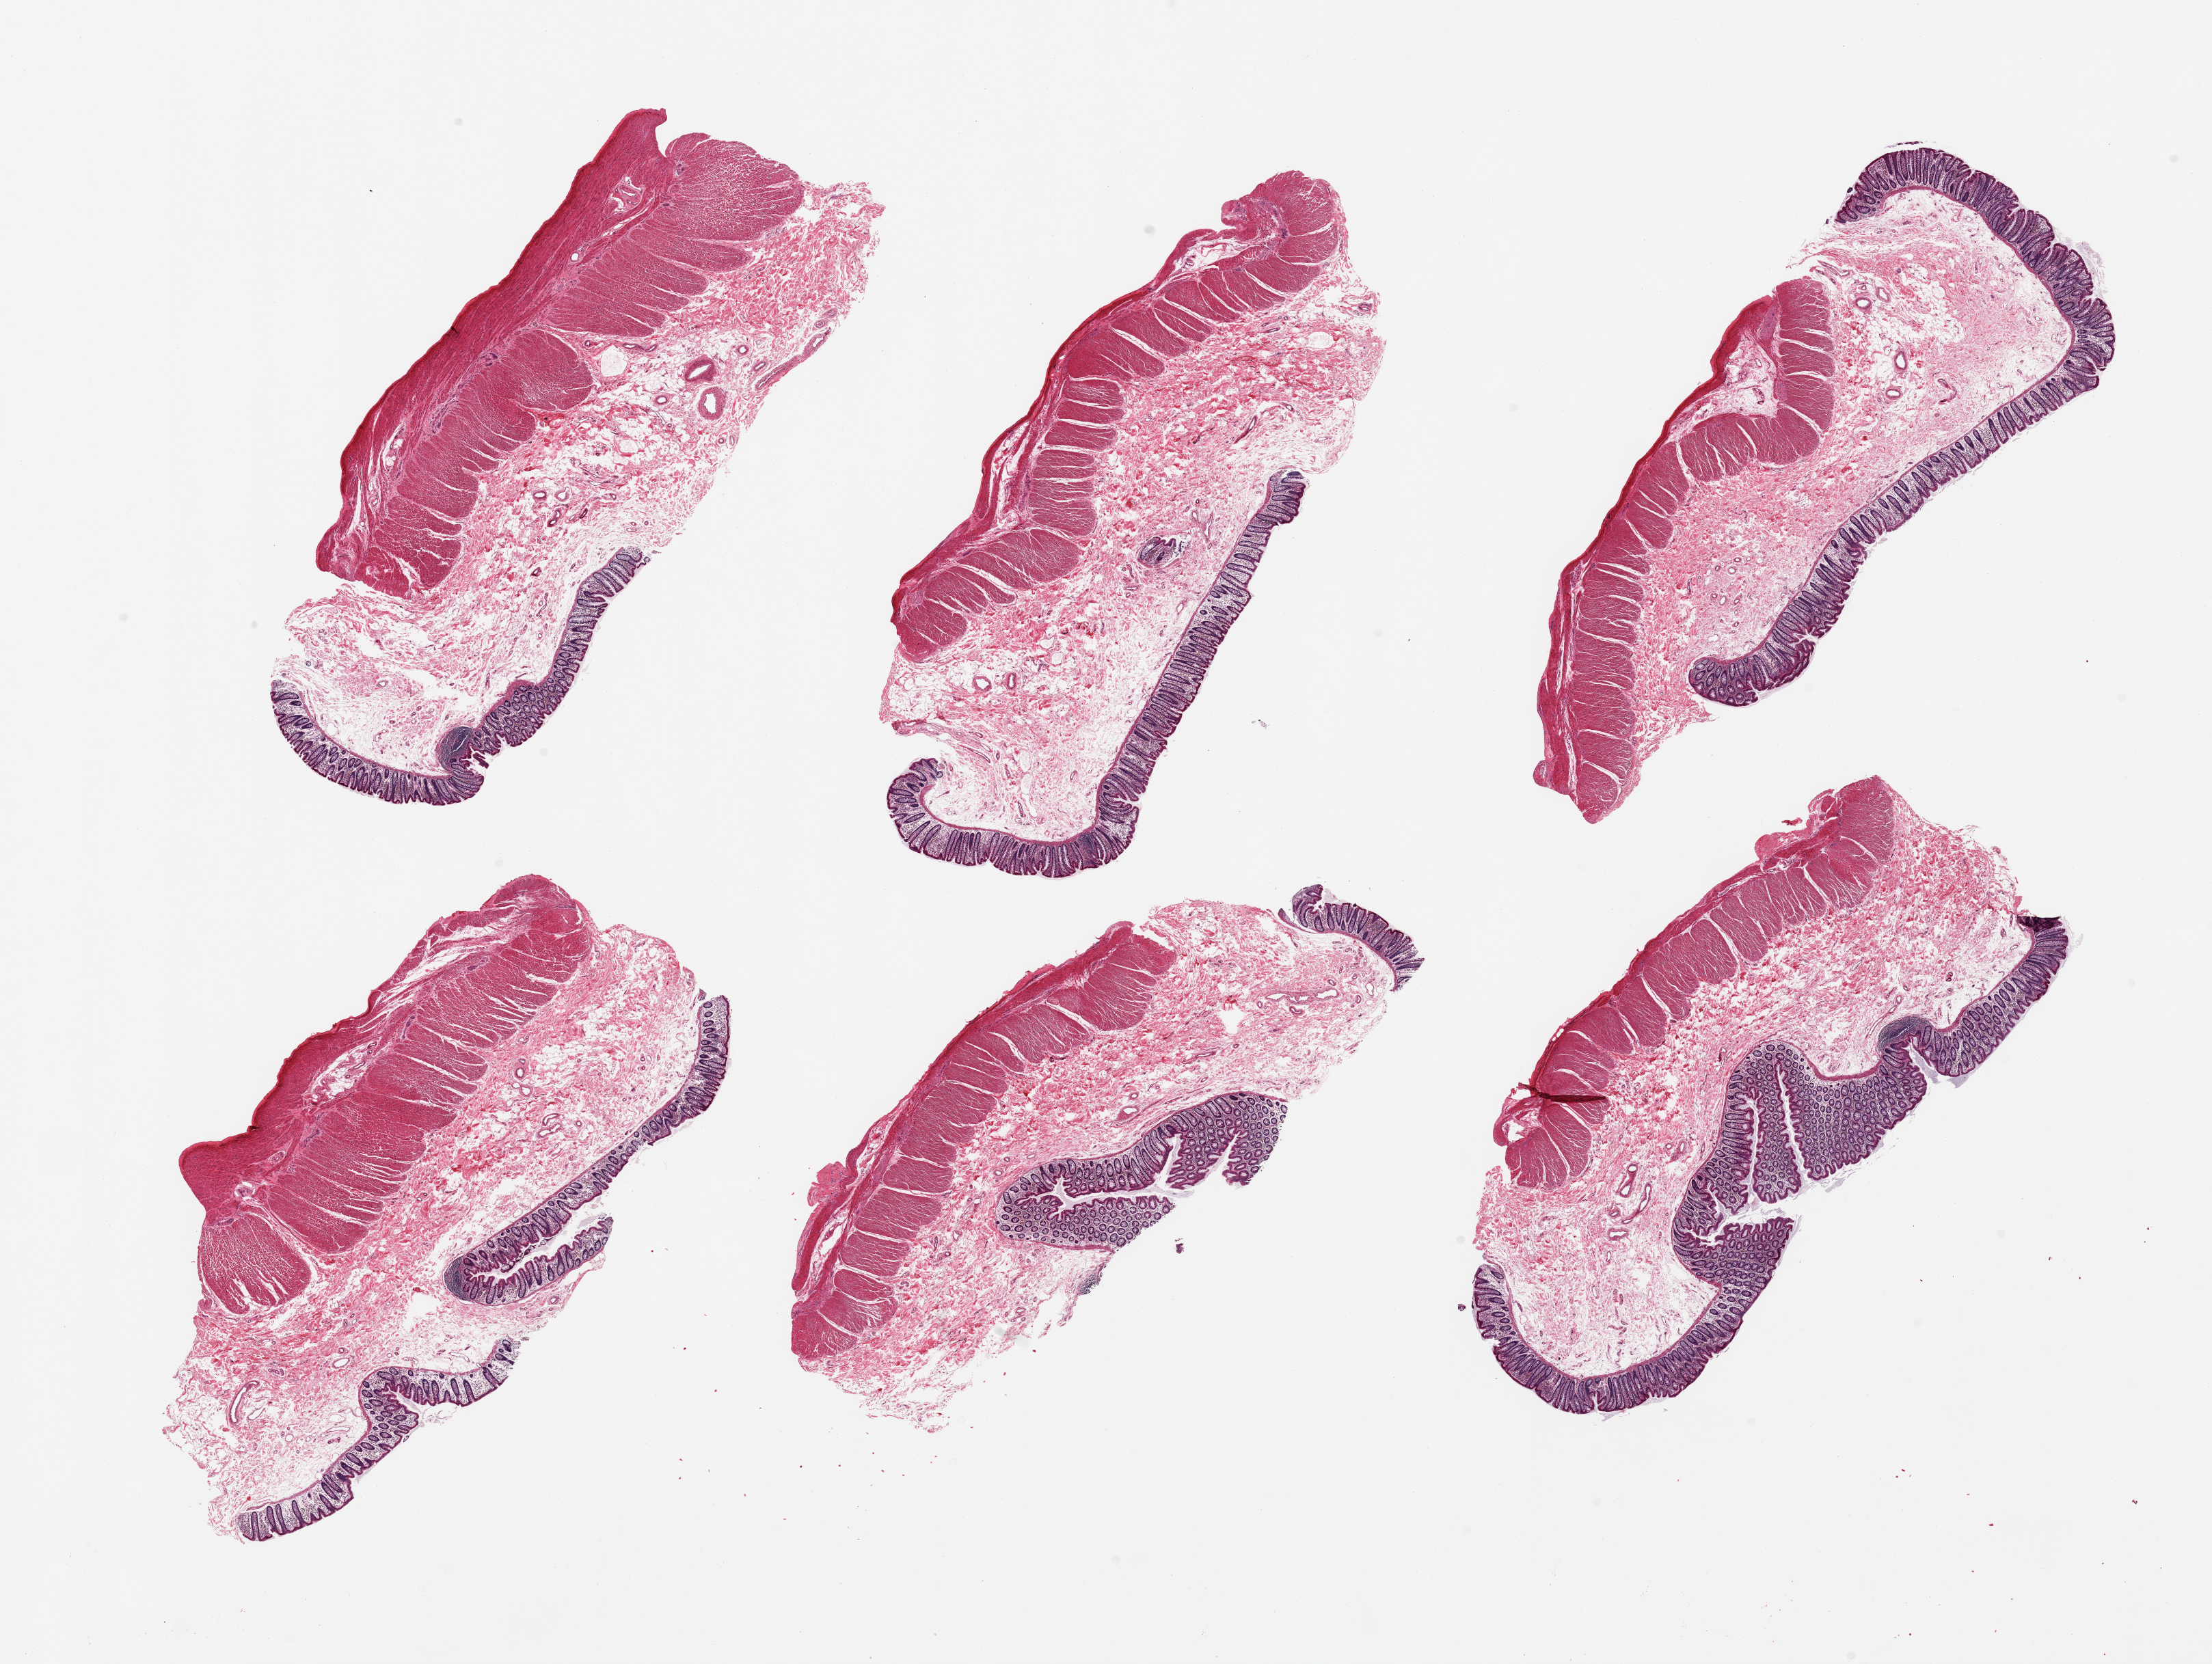
Digitized H&E-stained section, low-resolution overview of the scanned area, about 25.6 x 19.3 mm (slide scanned at 20x), PAXgene-fixed paraffin-embedded (PFPE) section, sampled site (target tissue): transverse colon, donor tissue sample. Donor: female.
* reviewer comment on this tissue sample: 6 pieces, well preserved; mucosa up to ~0.5mm, 10-15% thickness